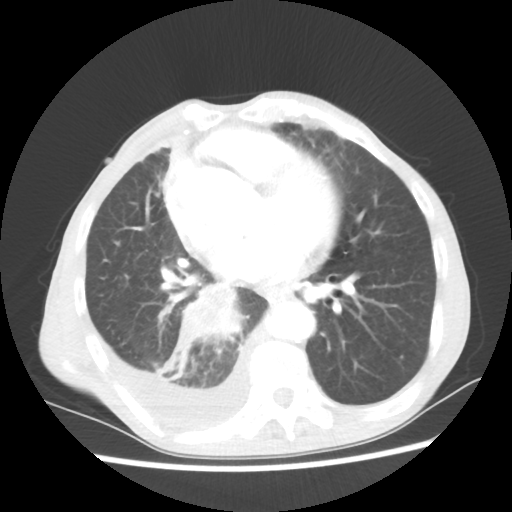
Chest CT, one axial slice; slice 26 of 60 in the series (ordered by position); lung window (W 1500 / L -600 HU); 5 mm slice thickness; 512 × 512 image matrix. Male patient, age 76 years. From the clinical record (not read from this slice): clinical TNM (as recorded): T3 N3 M1a; histopathological grade: G3.
Structures marked on this image (rectangle marked by the reading radiologist):
- lung tumour (recorded histology: squamous cell carcinoma): bounding box (x1, y1, x2, y2) in pixels: (159, 282, 251, 383)